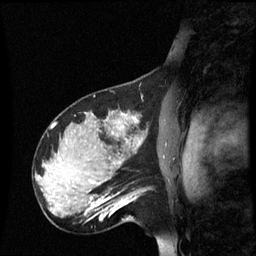
Breast MRI (dynamic contrast-enhanced), one sagittal slice. Position 42 of 60 along the scan axis. Dynamic contrast-enhanced series, image 2 of 3 at this slice position (ordered by acquisition). 1.5 T. TE 4.2 ms, TR 8.9 ms. 256 × 256 image matrix, field of view 220 × 220 mm. Patient: female, 31 years. From the clinical record (not read from this slice): setting: breast cancer imaged before/during neoadjuvant chemotherapy; receptor status: HR-positive, HER2-negative.
Annotated regions visible in this slice (semi-automatically segmented with operator editing):
- analysis volume of interest (the breast-tissue region the enhancement analysis was run in; not a lesion): bounding box (x1, y1, x2, y2) in pixels: (90, 180, 140, 223)
- tumour enhancement mask (voxels above the 70 % enhancement threshold inside the analysis volume of interest): (90, 196, 137, 221)